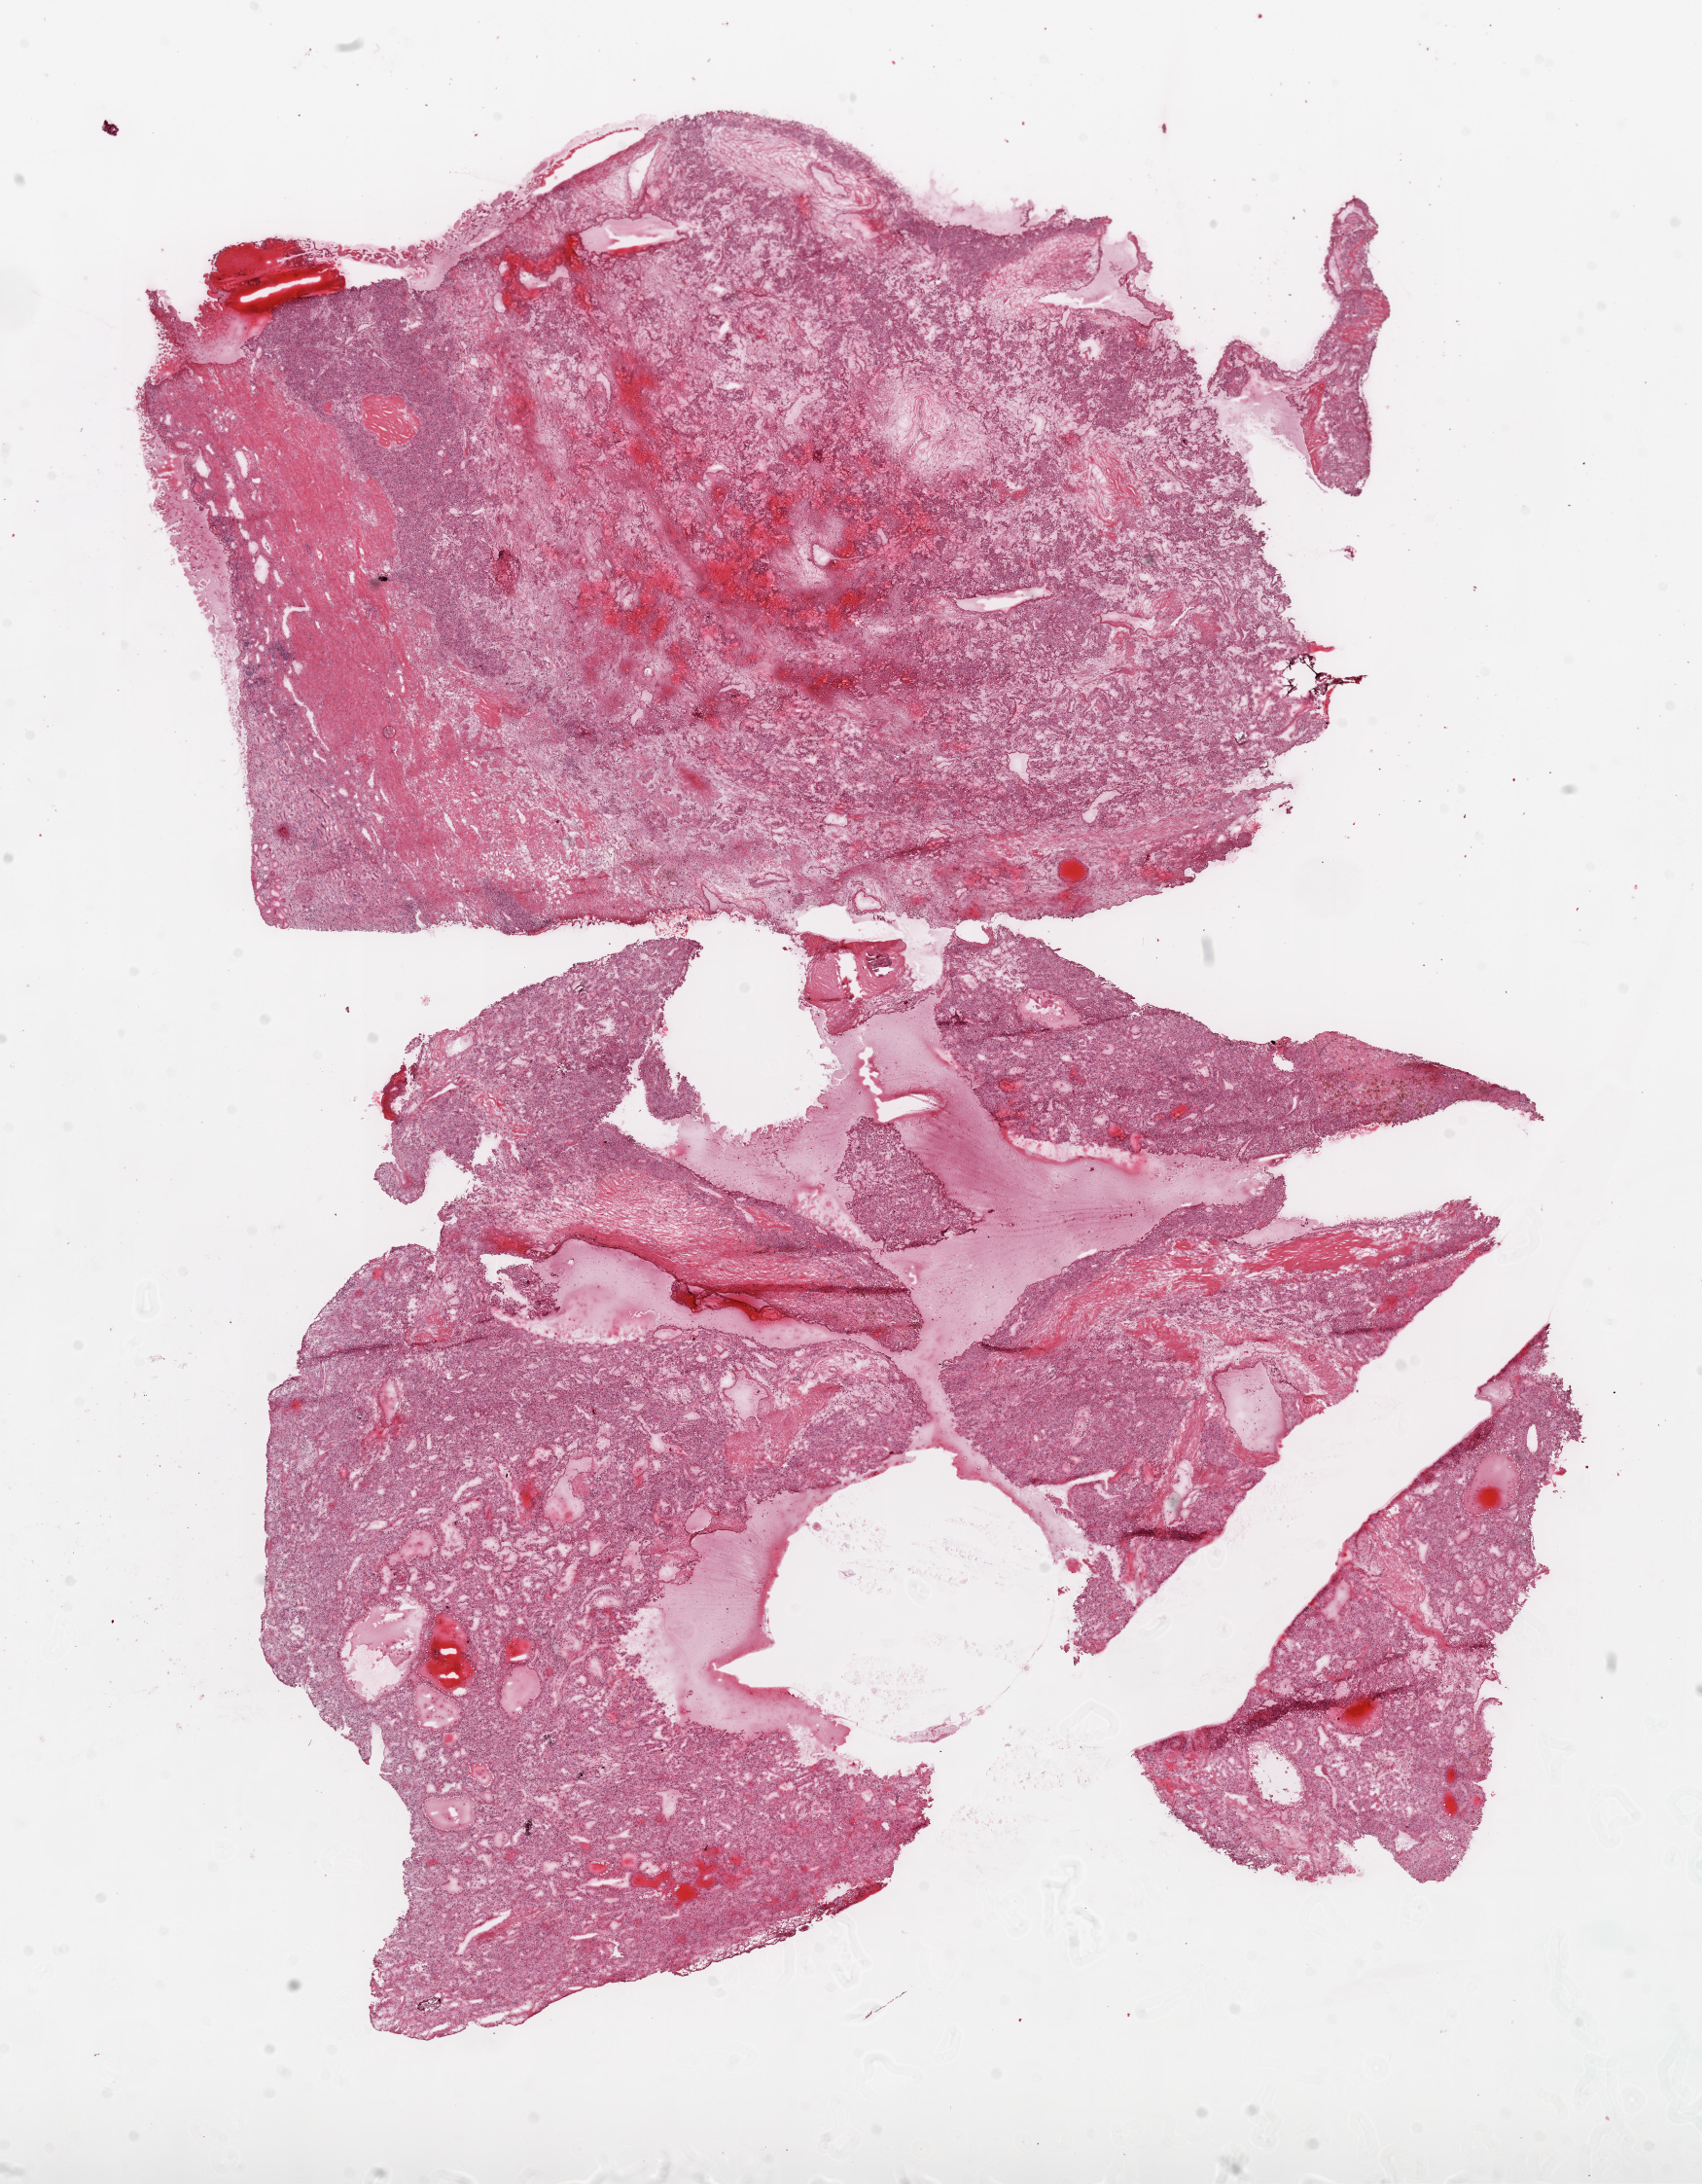
Whole-slide histology image, Hematoxylin and eosin (H&E) stained — low-resolution overview of the scanned area, about 14.0 x 18.0 mm (slide scanned at 20x). Frozen section. Primary tumour sample from the kidney. Patient: male, age at initial diagnosis 49 years. Histologic grade: G3 (poorly differentiated). Slide review estimates, as recorded: tumour cells 80%, tumour nuclei 80%, normal cells 0%, stromal cells 20%, necrosis 0%.
AJCC pathologic stage: I. Diagnosis: Clear cell adenocarcinoma, NOS. Laterality: right.